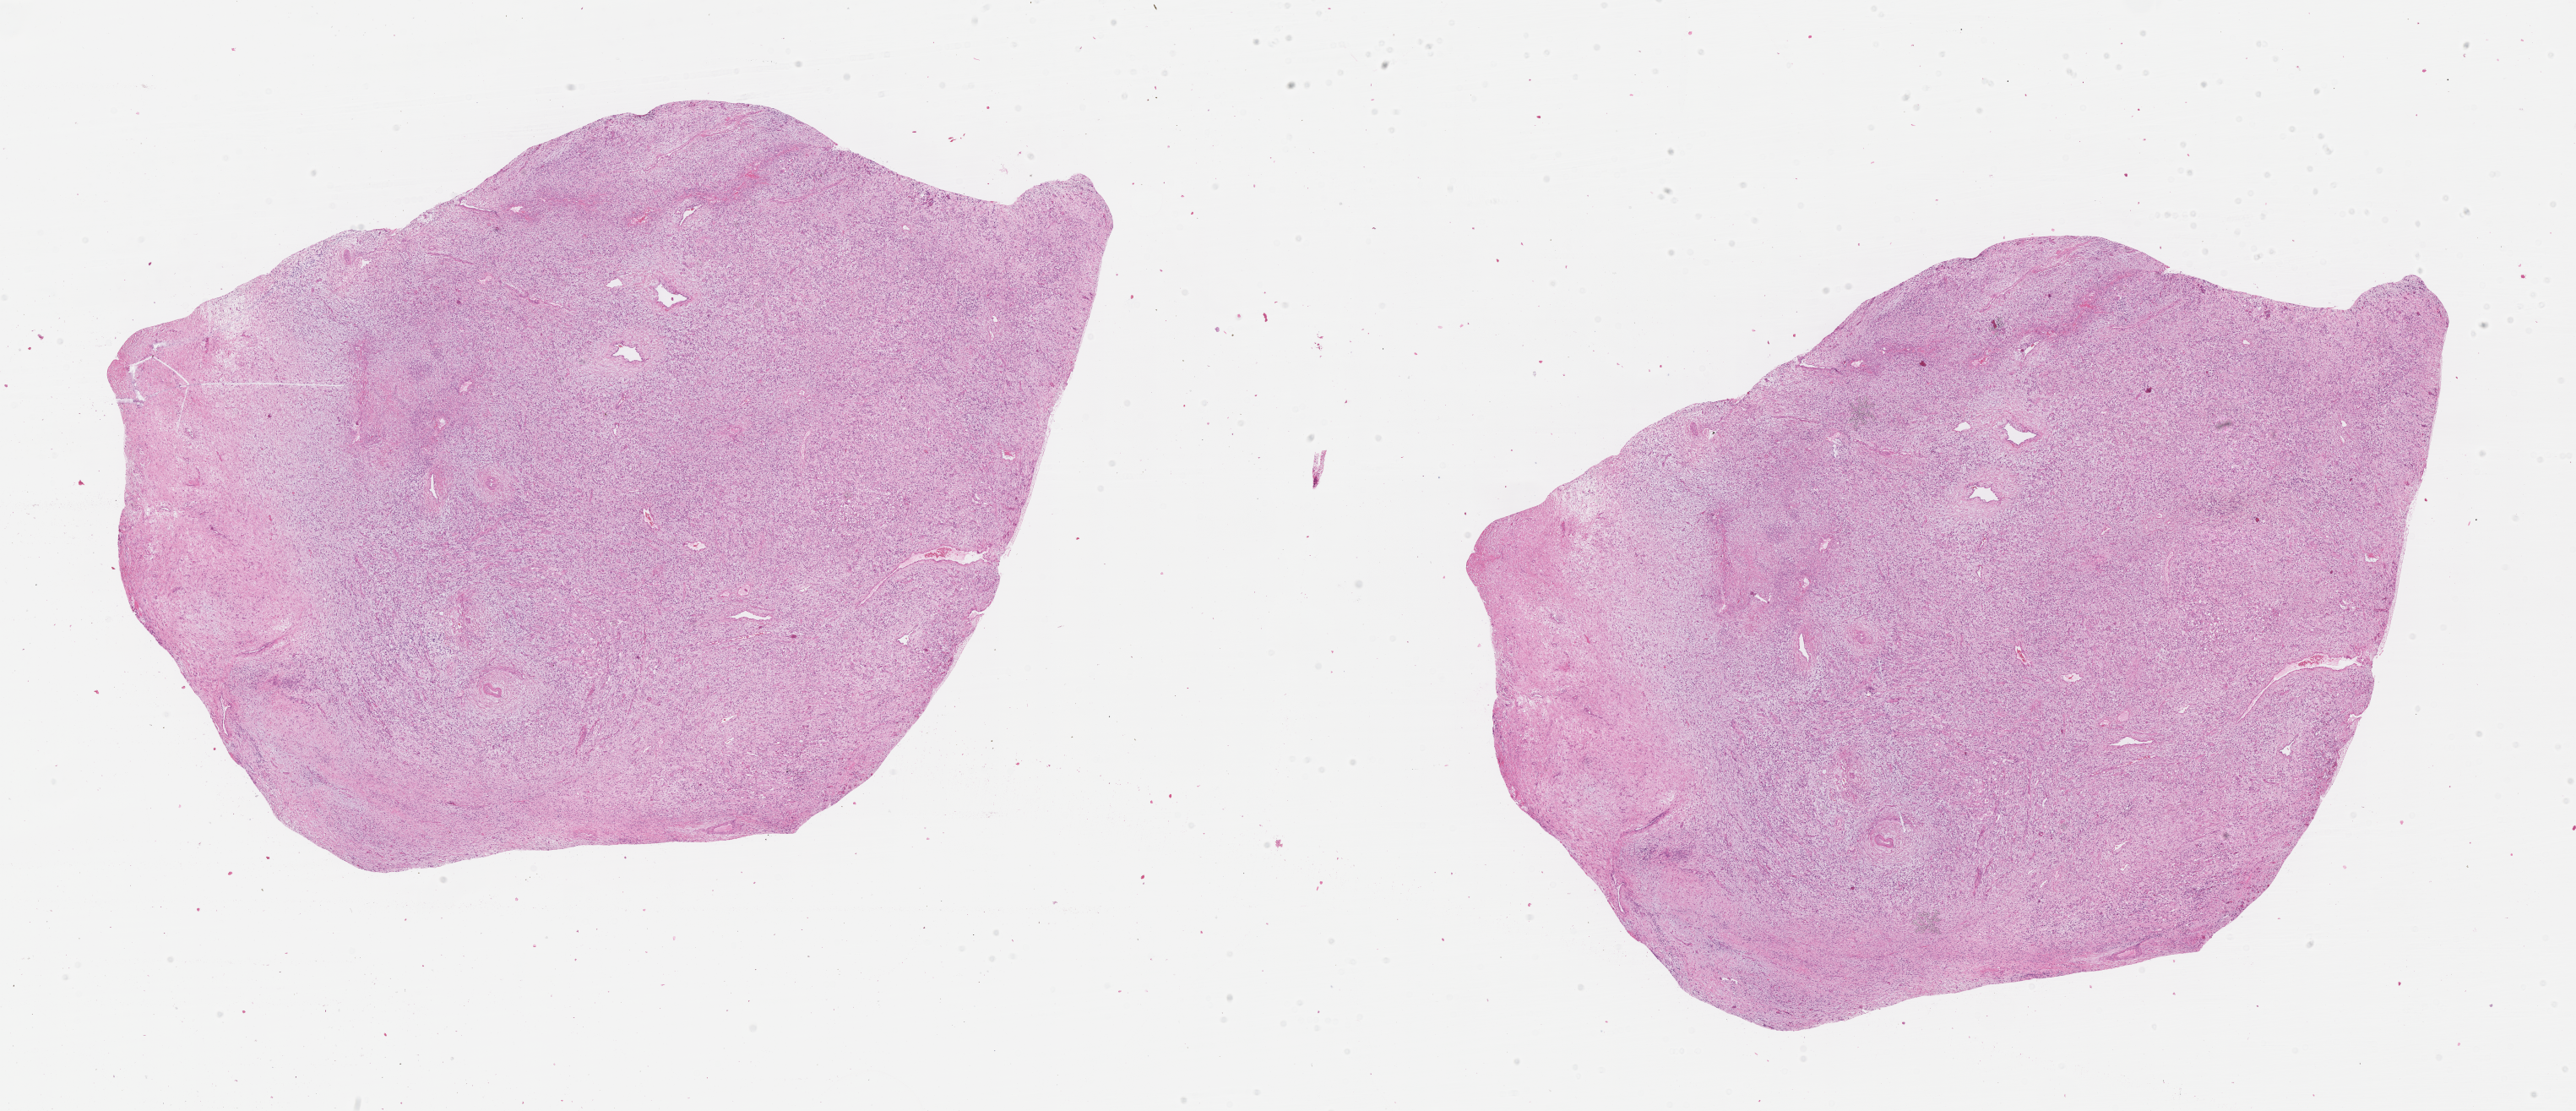
Whole-slide image, haematoxylin and eosin stain of tumor tissue, whole scanned area (about 24.7 x 10.6 mm) shown as a low-resolution overview; formalin-fixed, paraffin-embedded (FFPE) tissue; sample anatomic site: abdomen. Patient: male, age 2.5 years at diagnosis.
* metastatic status at presentation (as recorded): non-metastatic
* stage (as recorded): 3
* diagnosis: rhabdomyosarcoma; histological classification: embryonal rhabdomyosarcoma